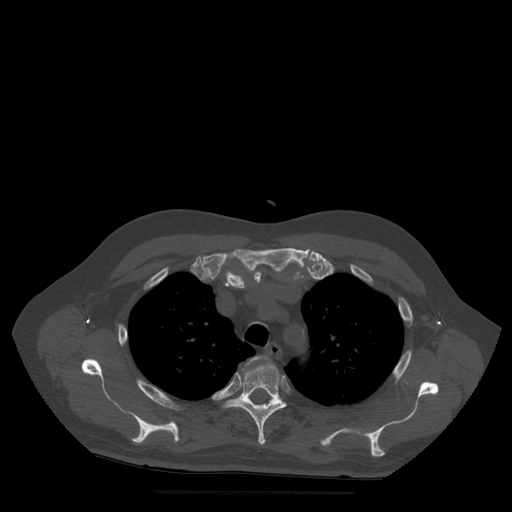
CT including the spine, one axial slice. Position 392 of 522 along the scan axis. Bone window (W 1800 / L 400 HU). 512 × 512 image matrix, field of view 420 × 420 mm. Patient age 72 years. Case-level facts recorded for this patient, not image findings: primary cancer: prostate.
Outlined on this slice (semi-automatic segmentation, software-assisted and operator-edited):
- T3 vertebra: bounding box (x1, y1, x2, y2) in pixels: (243, 357, 259, 372)
- T4 vertebra: (225, 363, 287, 445)